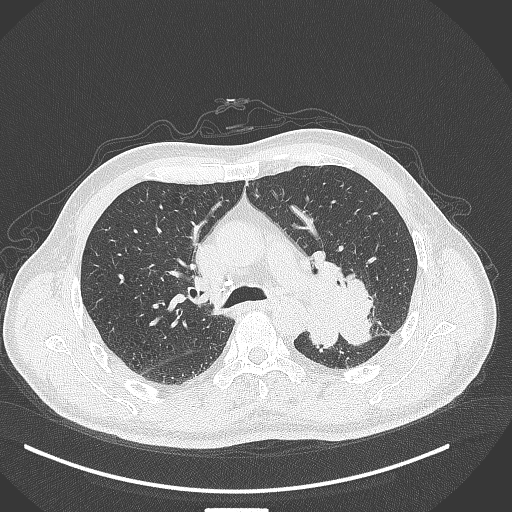
Chest CT, one axial slice. Position 277 of 429 along the scan axis. Reconstruction kernel B70f. Lung window (W 1500 / L -600 HU). 1 mm slice thickness. 512 × 512 image matrix, field of view 400 × 400 mm. Male patient, age 55 years. From the clinical record (not read from this slice): clinical TNM (as recorded): T3 N0 M1c; histopathological grade: G3.
Outlined on this slice (rectangle marked by the reading radiologist):
- lung tumour (recorded histology: adenocarcinoma): box from (x=307, y=253) to (x=381, y=357) px